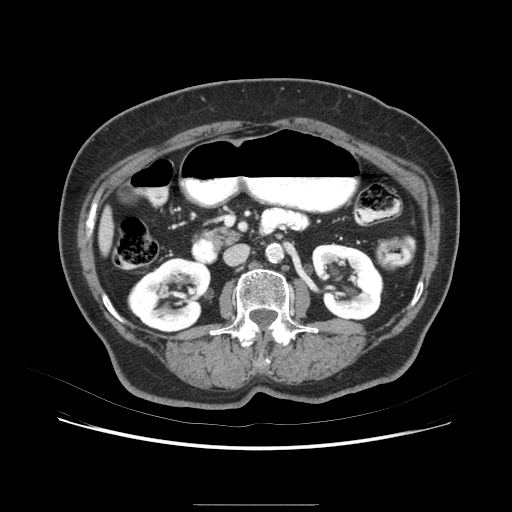
Contrast-enhanced abdominal CT (liver protocol), one axial slice; position 21 of 79 along the scan axis; soft-tissue window (W 400 / L 40 HU); 512 × 512 image matrix, field of view 380 × 380 mm. From the clinical record (not read from this slice): diagnosis: hepatocellular carcinoma (patient treated with transarterial chemoembolisation; whether this scan precedes or follows treatment is not stated here); TNM stage (as recorded): Stage-I.
Structures marked on this image (semi-automatically segmented with operator editing):
- liver parenchyma outside the tumour (the mass and vessels are separate outlines, so this box may not span the whole liver): bounding box <96,195,130,276> (left, top, right, bottom; pixels)